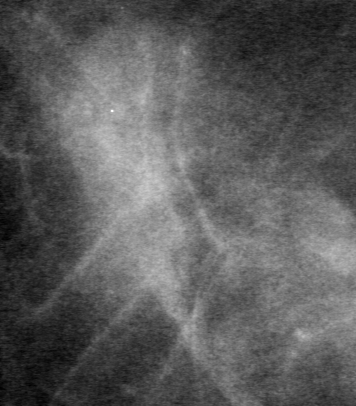
Cropped region of a digitized screen-film mammogram centred on a radiologist-marked abnormality; right breast; MLO view.
Mass, shape lobulated, margins obscured; BI-RADS assessment category 0; subtlety rating 2 on a 1 (subtle) to 5 (obvious) scale; pathology (as recorded): benign.